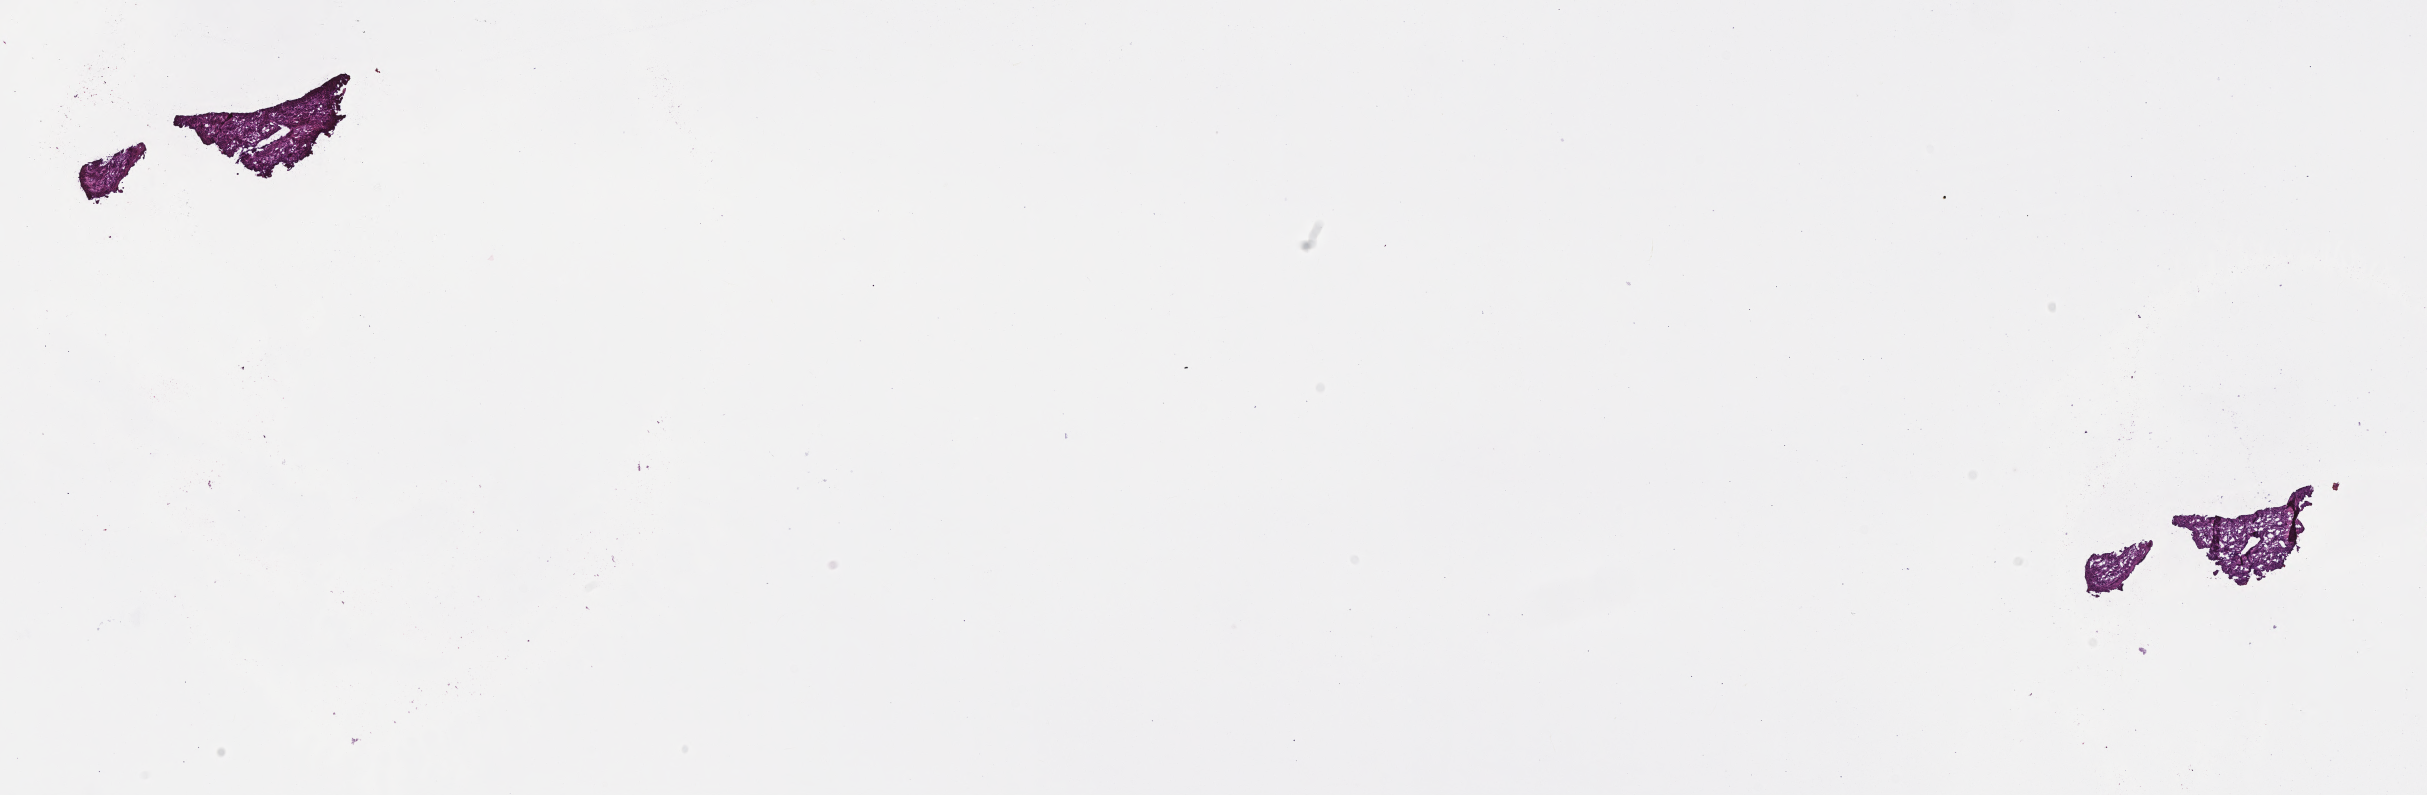
Digitized hematoxylin and eosin (H&E)-stained section of tumor tissue from the retroperitoneum, a low-resolution overview of the entire scanned area, about 19.6 x 6.4 mm, cryosection (OCT / tissue freezing medium). Patient: female, age 60 days.
Recorded diagnosis: Neuroblastoma, NOS.